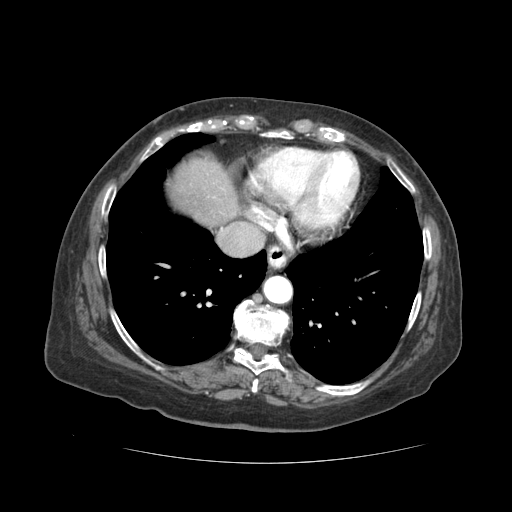
Contrast-enhanced abdominal CT (liver protocol), one axial slice; position 47 of 59 along the scan axis; reconstruction kernel STANDARD; 120 kVp; soft-tissue window (W 400 / L 40 HU); 512 × 512 image matrix, field of view 380 × 380 mm. From the clinical record (not read from this slice): diagnosis: hepatocellular carcinoma (patient treated with transarterial chemoembolisation; whether this scan precedes or follows treatment is not stated here); TNM stage (as recorded): Stage-I; Child-Pugh class: A.
Outlined on this slice (semi-automatic segmentation, software-assisted and operator-edited):
- liver parenchyma outside the tumour (the mass and vessels are separate outlines, so this box may not span the whole liver): bounding box (x1, y1, x2, y2) in pixels: (170, 158, 238, 224)